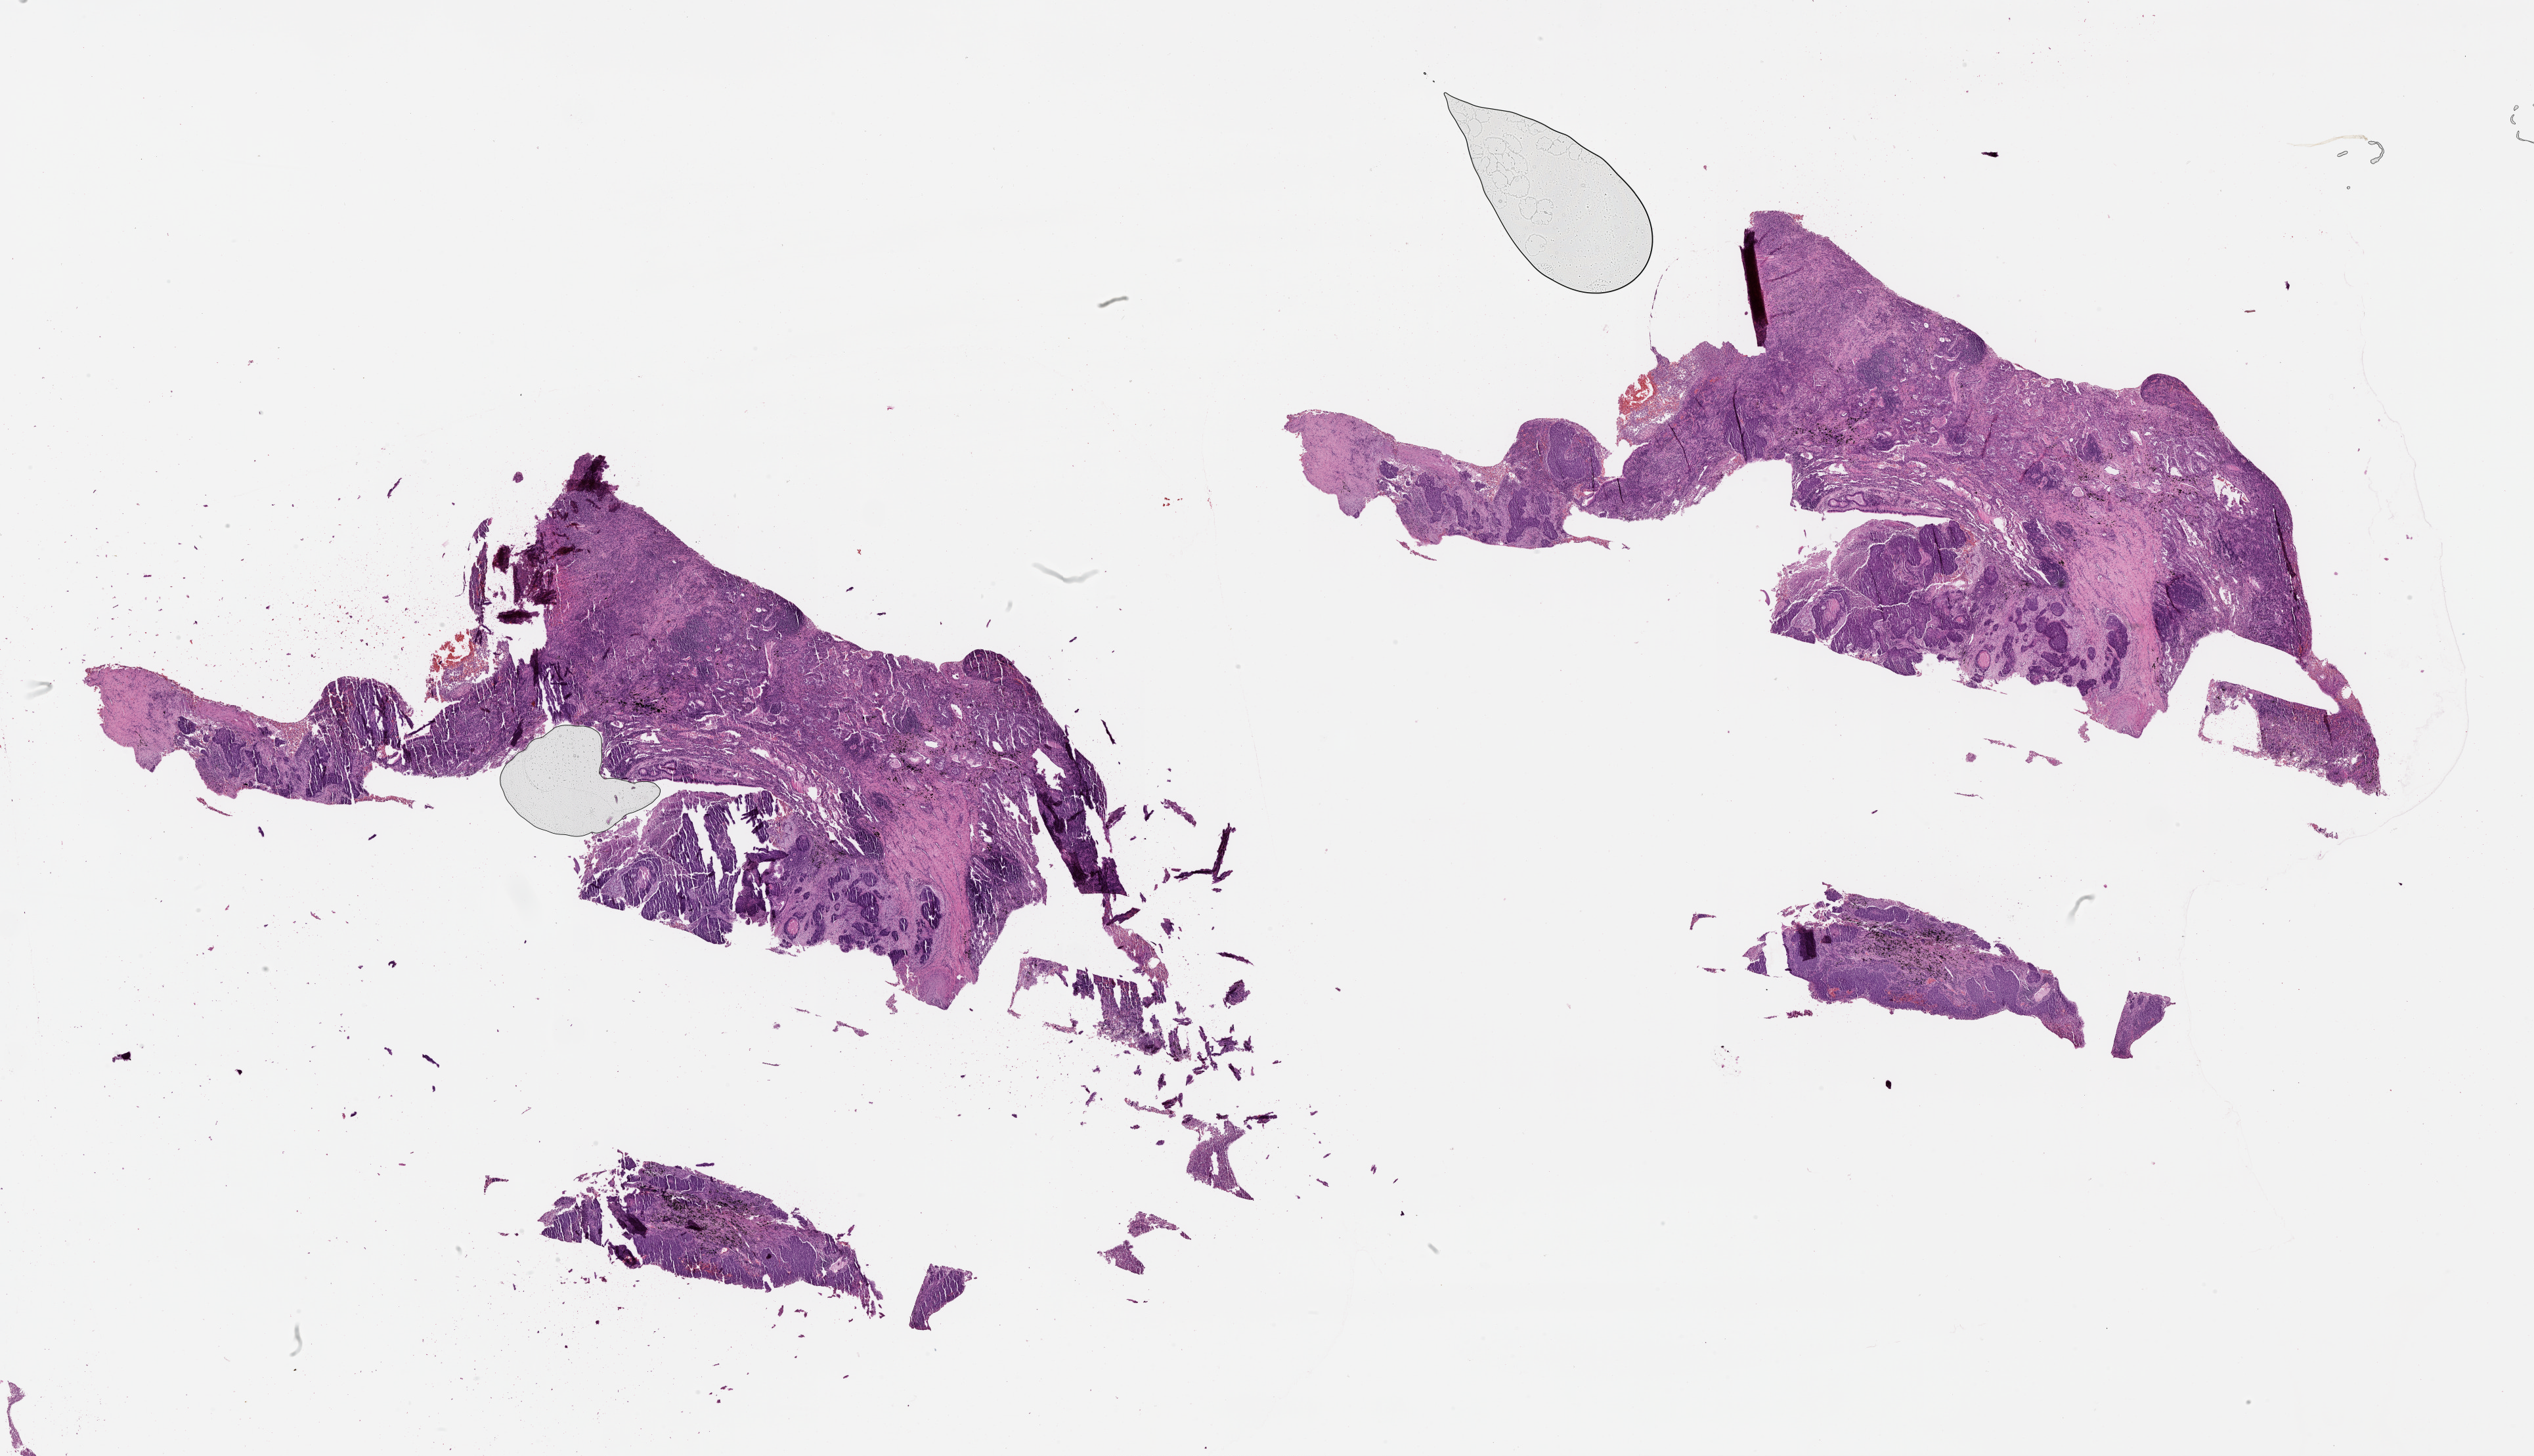
Digitized Hematoxylin and eosin (H&E) stained tissue section (whole slide), a low-resolution overview of the entire scanned area, about 31.1 x 17.9 mm (from a 20x scan); tumour tissue sample, lung. Patient: male, age 59 years.
Patient diagnosis (cohort enrolment): squamous cell carcinoma (lung).